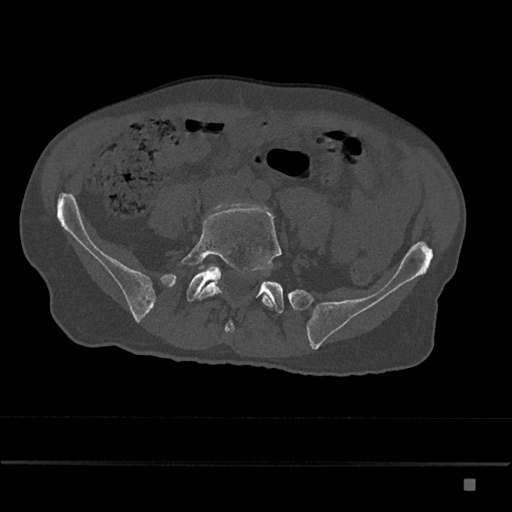
CT including the spine, one axial slice; slice 264 of 797 in the series (ordered by position); bone window (W 1800 / L 400 HU); 0.5 mm slice thickness; 512 × 512 image matrix, field of view 390 × 390 mm. Patient: male, 72 years. From the clinical record (not read from this slice): primary cancer: prostate.
Annotated regions visible in this slice (semi-automatically segmented with operator editing):
- L5 vertebra: bounding box [x1, y1, x2, y2] px = [181, 207, 282, 308]